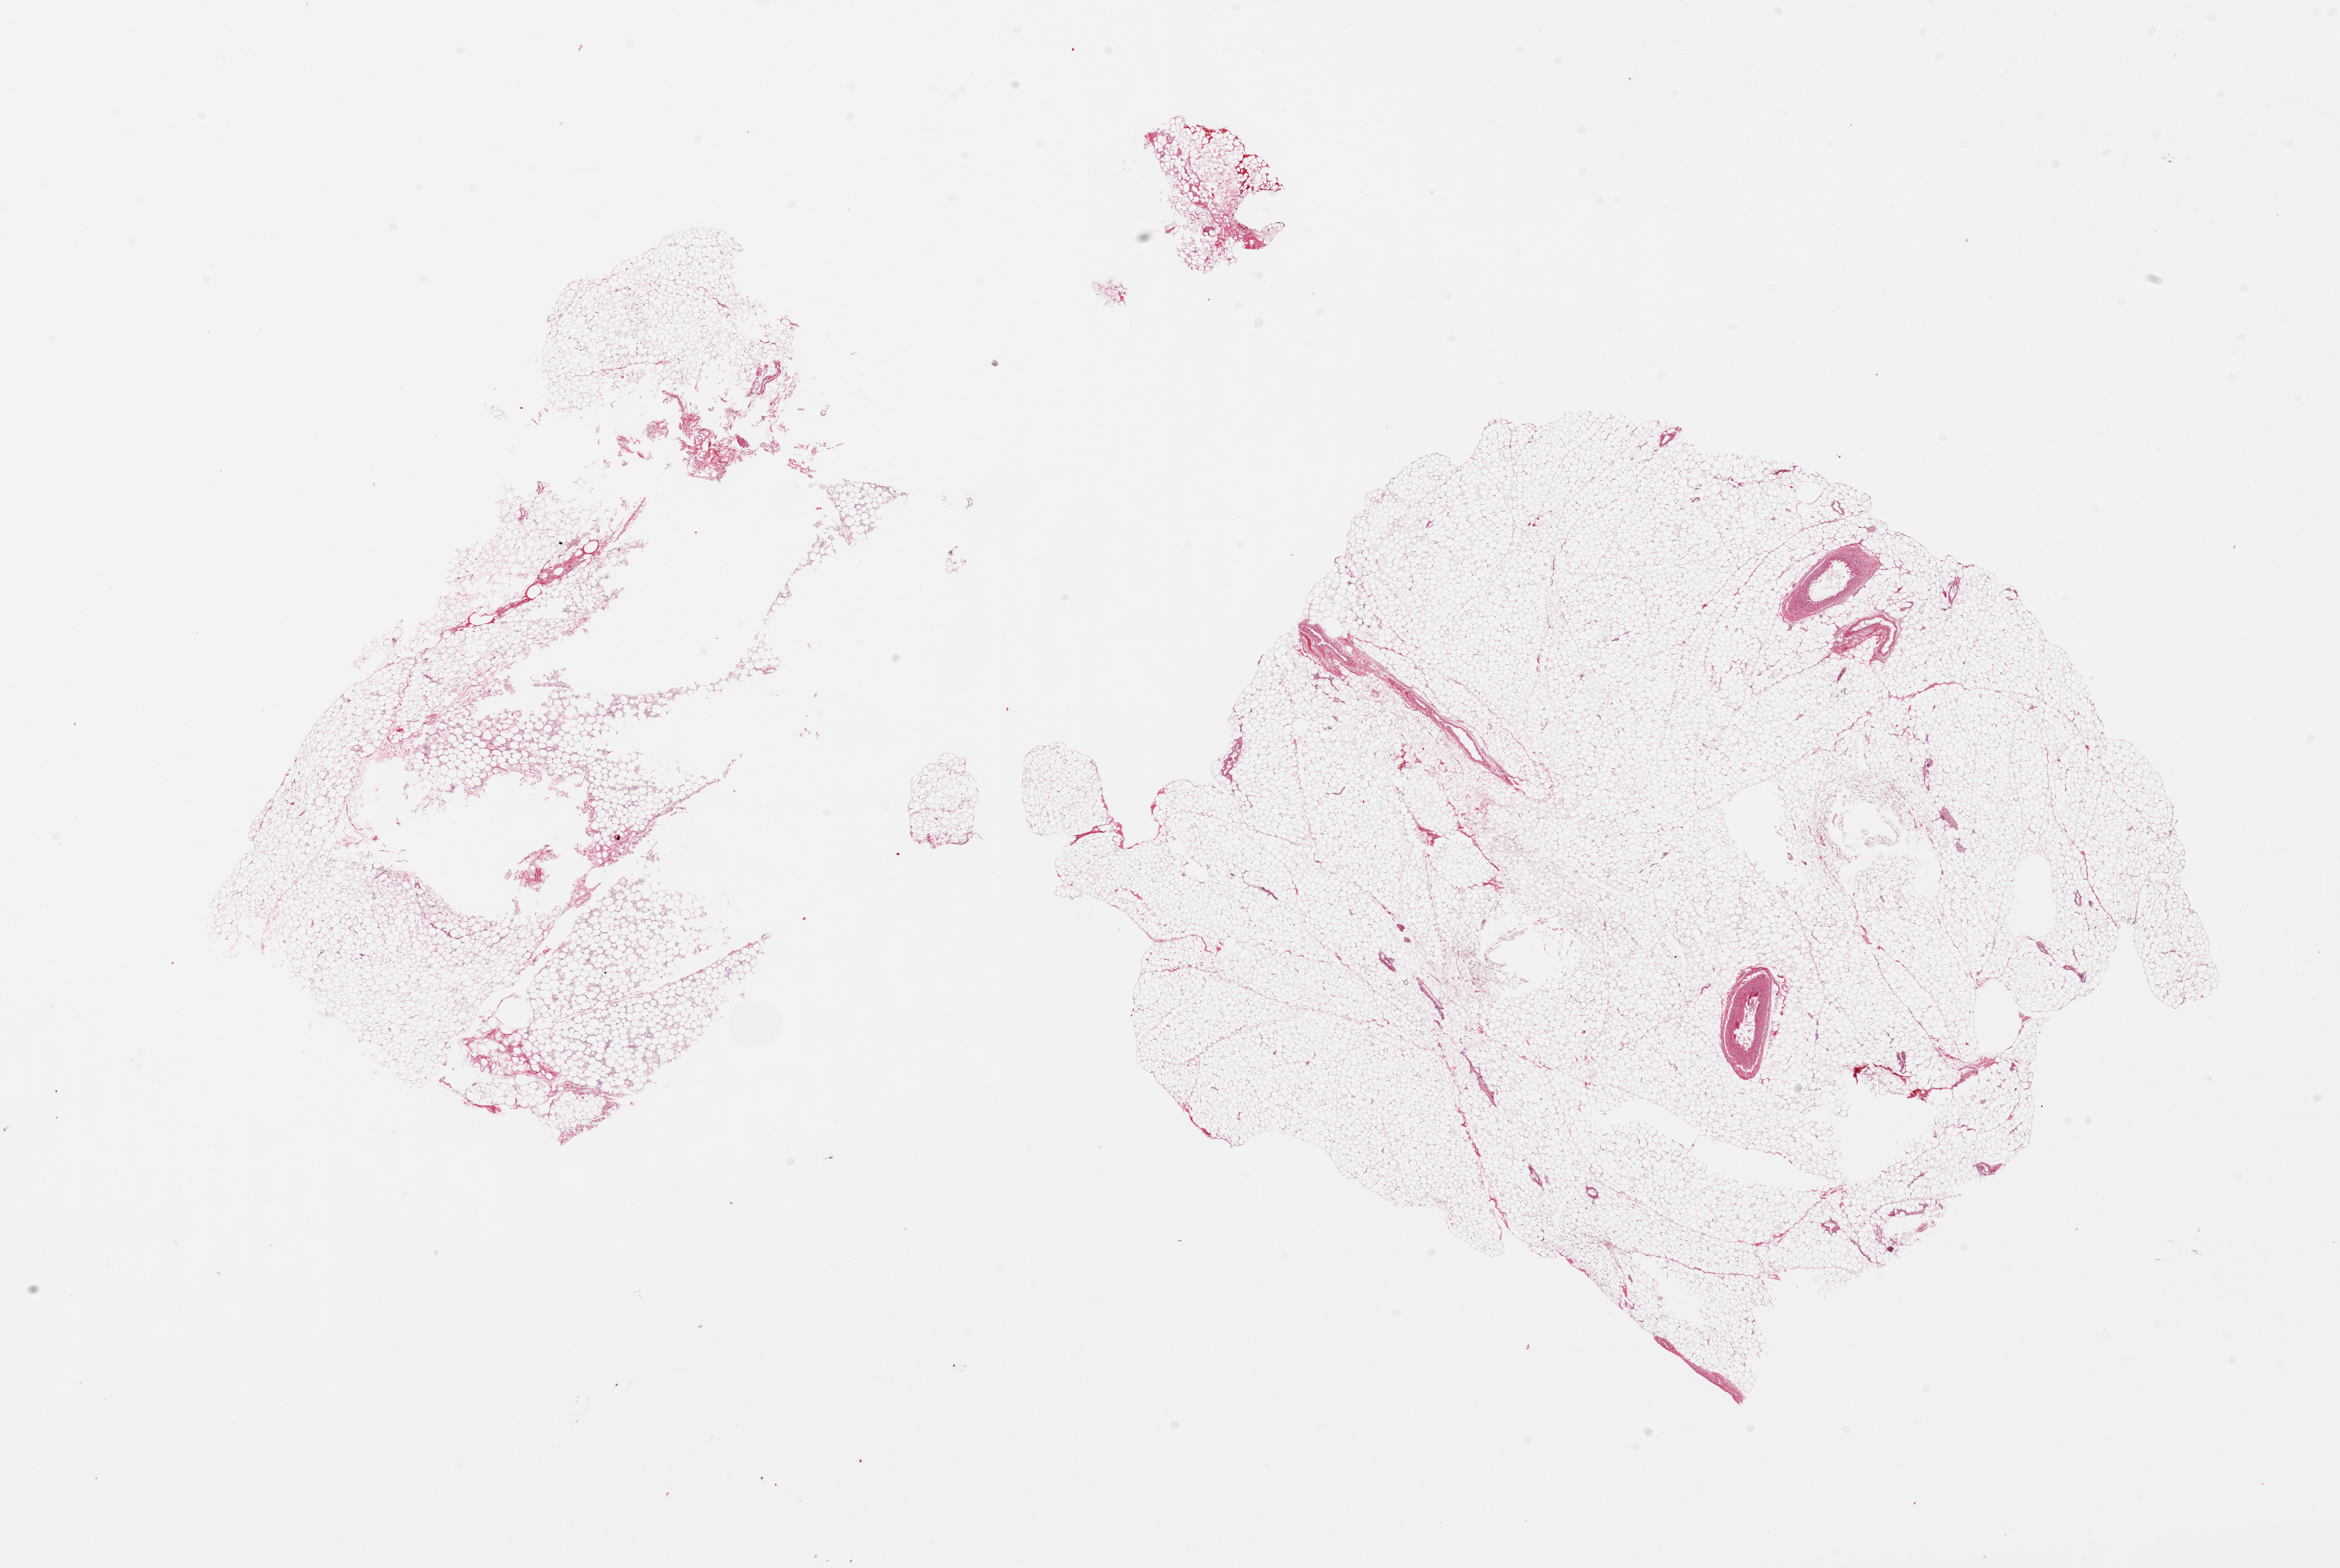
H&E whole-slide image — a low-resolution overview of the entire scanned area, about 27.6 x 18.5 mm. Donor: male.
- specimen: PAXgene-fixed, paraffin-embedded tissue; sampled site (target tissue): omentum; tissue donor sample